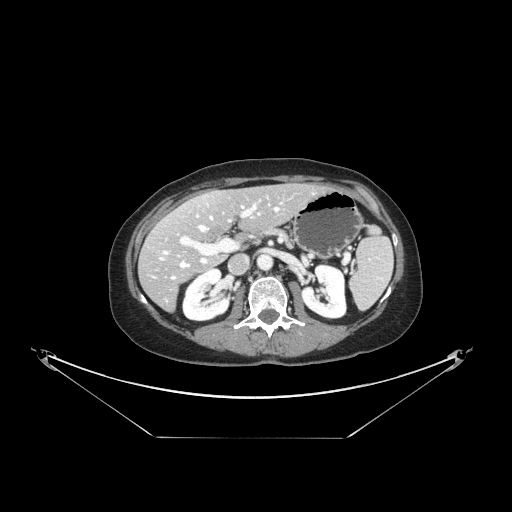
Contrast-enhanced abdominal CT, one axial slice; reconstruction kernel STANDARD; 120 kVp; intravenous contrast given; soft-tissue window (W 400 / L 40 HU); 2.5 mm slice thickness; 512 × 512 image matrix. Female patient, age 73 years. From the clinical record (not read from this slice): diagnosis: colorectal cancer liver metastases, imaged before liver resection; multiple liver metastases: no; largest metastasis: 1 cm; disease in both lobes: no.
Annotated regions visible in this slice (outlined manually by an expert reader):
- hepatic veins: bounding box <161,205,279,279> (left, top, right, bottom; pixels)
- liver: <140,184,323,310>
- planned liver remnant (the part of the liver to remain after resection): <168,184,323,239>
- portal vein (with intrahepatic branches): <180,204,257,264>